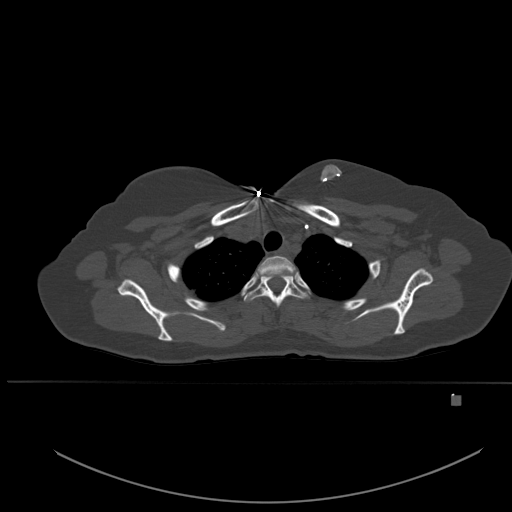
CT including the spine, one axial slice. Bone window (W 1800 / L 400 HU). 512 × 512 image matrix, field of view 443 × 443 mm. Female patient, age 49 years. From the clinical record (not read from this slice): primary cancer: breast.
Annotated regions visible in this slice (semi-automatic segmentation, software-assisted and operator-edited):
- T1 vertebra: box from (x=257, y=256) to (x=296, y=277) px
- T2 vertebra: (x=244, y=271)–(x=308, y=307)